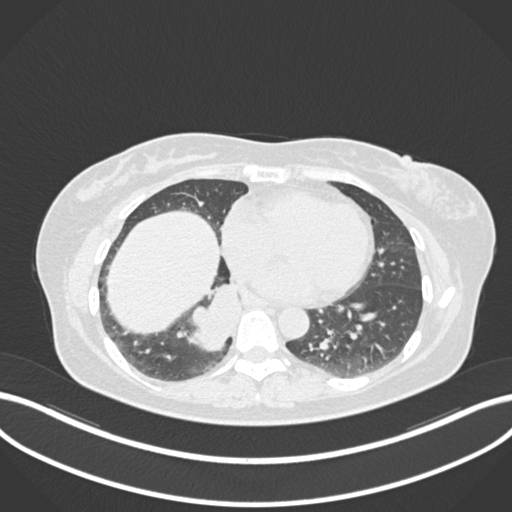
Chest CT, one axial slice. Slice 554 of 677 in the series (ordered by position). Reconstruction kernel B30f. 120 kVp. Lung window (W 1500 / L -600 HU). 1 mm slice thickness. 512 × 512 image matrix, field of view 400 × 400 mm. Female patient, age 54 years. Case-level facts recorded for this patient, not image findings: clinical TNM (as recorded): T4 N0 M0.
Structures marked on this image (bounding box drawn by a radiologist):
- lung tumour (recorded histology: adenocarcinoma): bounding box (x1, y1, x2, y2) in pixels: (181, 277, 240, 353)